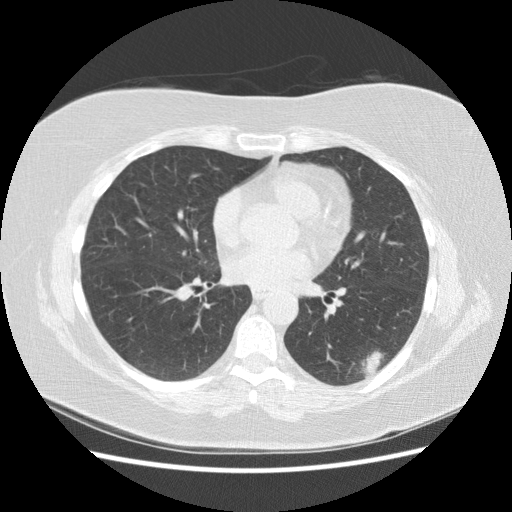
Chest CT (low-dose screening protocol), one axial image; third annual screen; lung window (W 1500 / L -600 HU); 2.5 mm slice thickness; standard (soft-tissue) reconstruction kernel (STANDARD); slice 74 of 151 in the series. Female participant, aged 57 years at enrolment. Current smoker at enrolment.
- Expert-annotated lung lesion, bounding box [x1, y1, x2, y2] px = [337, 324, 405, 389].
- Reader record for this screening exam (exam-level; its link to the box is not recorded): non-calcified nodule or mass ≥4 mm, left lower lobe, 40 × 20 mm, poorly defined margins, mixed attenuation, pre-existing on the prior screen: yes; interval growth: yes.
- Official screen result: positive, other.
- Later outcome: lung cancer diagnosed 55 days after this screen — squamous cell carcinoma, NOS, left lower lobe, poorly differentiated (G3), stage IB (AJCC 6th edition), 40 mm at pathology.